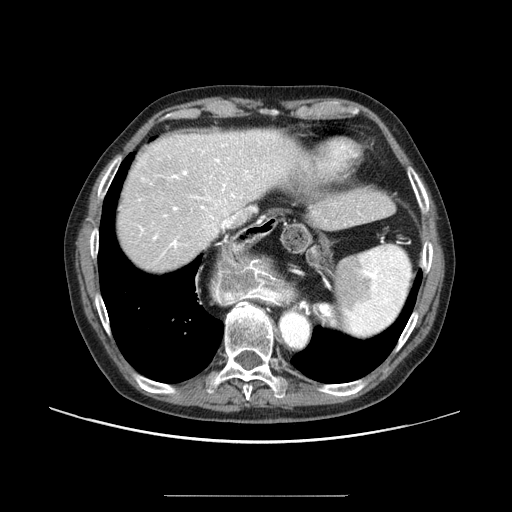
Contrast-enhanced abdominal CT (liver protocol), one axial slice. Position 73 of 91 along the scan axis. Reconstruction kernel STANDARD. One of 2 acquisitions stored at this slice position. Soft-tissue window (W 400 / L 40 HU). 2.5 mm slice thickness. 512 × 512 image matrix, field of view 400 × 400 mm. From the clinical record (not read from this slice): diagnosis: hepatocellular carcinoma (patient treated with transarterial chemoembolisation; whether this scan precedes or follows treatment is not stated here); TNM stage (as recorded): Stage-I; Child-Pugh class: A; tumour differentiation: moderately differentiated.
Annotated regions visible in this slice (semi-automatically segmented with operator editing):
- abdominal aorta: bounding box <281,313,307,346> (left, top, right, bottom; pixels)
- liver parenchyma outside the tumour (the mass and vessels are separate outlines, so this box may not span the whole liver): <118,130,298,270>
- liver vessels: <139,135,269,256>